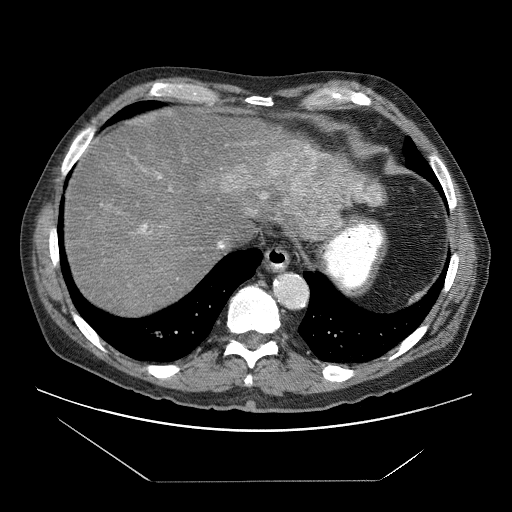
Contrast-enhanced abdominal CT (liver protocol), one axial slice; slice 61 of 83 in the series (ordered by position); reconstruction kernel STANDARD; 120 kVp; soft-tissue window (W 400 / L 40 HU); 512 × 512 image matrix. From the clinical record (not read from this slice): diagnosis: hepatocellular carcinoma (patient treated with transarterial chemoembolisation; whether this scan precedes or follows treatment is not stated here); TNM stage (as recorded): Stage-IVB; Child-Pugh class: B; tumour differentiation: poorly differentiated; tumour nodularity: uninodular.
Structures marked on this image (semi-automatically segmented with operator editing):
- liver parenchyma outside the tumour (the mass and vessels are separate outlines, so this box may not span the whole liver): bounding box [x1, y1, x2, y2] px = [64, 112, 382, 314]
- mass: [219, 140, 383, 240]
- liver vessels: [138, 145, 309, 249]